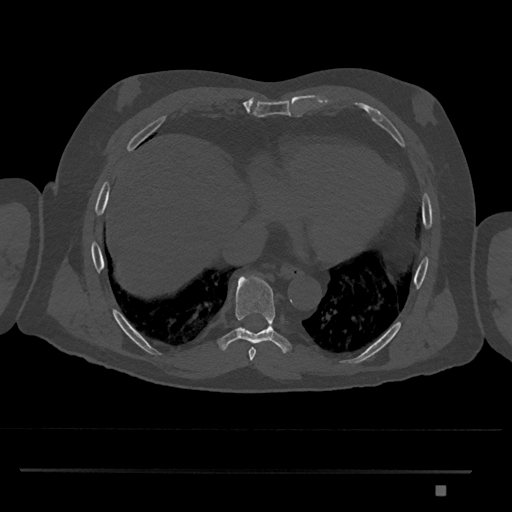
CT including the spine, one axial slice; slice 1113 of 1134 in the series (ordered by position); reconstruction kernel Br40s/3; bone window (W 1800 / L 400 HU); 0.5 mm slice thickness; 512 × 512 image matrix, field of view 429 × 429 mm. Patient: male, 65 years. Case-level facts recorded for this patient, not image findings: primary cancer: prostate.
Structures marked on this image (semi-automatic segmentation, software-assisted and operator-edited):
- T8 vertebra: box from (x=218, y=275) to (x=292, y=353) px